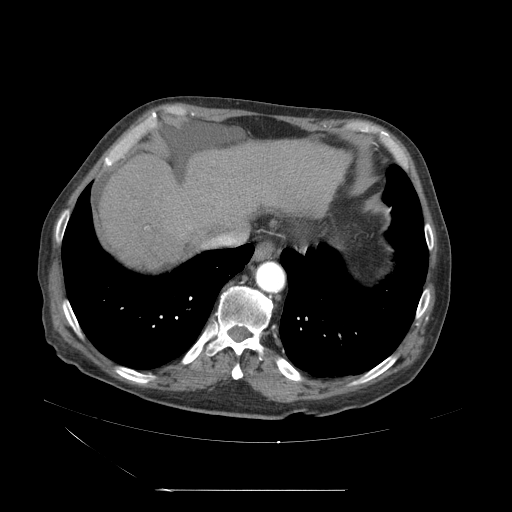
Contrast-enhanced abdominal CT (liver protocol), one axial slice; slice 51 of 71 in the series (ordered by position); reconstruction kernel STANDARD; 120 kVp; soft-tissue window (W 400 / L 40 HU); 2.5 mm slice thickness; 512 × 512 image matrix. From the clinical record (not read from this slice): diagnosis: hepatocellular carcinoma (patient treated with transarterial chemoembolisation; whether this scan precedes or follows treatment is not stated here); TNM stage (as recorded): Stage-II; Child-Pugh class: A; tumour size: 1 cm.
Outlined on this slice (semi-automatically segmented with operator editing):
- abdominal aorta: bounding box (x1, y1, x2, y2) in pixels: (255, 263, 285, 294)
- liver parenchyma outside the tumour (the mass and vessels are separate outlines, so this box may not span the whole liver): (108, 125, 346, 272)
- liver vessels: (110, 196, 245, 255)